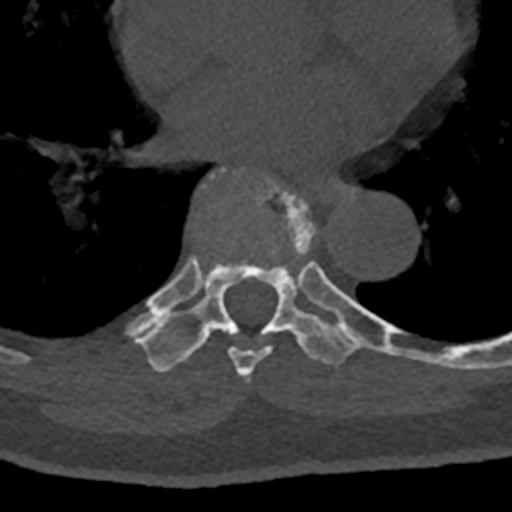
CT including the spine, one axial slice; position 731 of 797 along the scan axis; reconstruction kernel Br40s/3; bone window (W 1800 / L 400 HU); 0.5 mm slice thickness; 512 × 512 image matrix. Male patient, age 74 years. From the clinical record (not read from this slice): primary cancer: renal; vertebrae with lytic lesions (as recorded): T10, L1, L2, L3, L4, L5.
Outlined on this slice (semi-automatic segmentation, software-assisted and operator-edited):
- T7 vertebra: bounding box [x1, y1, x2, y2] px = [208, 169, 354, 380]
- T8 vertebra: [131, 229, 432, 372]